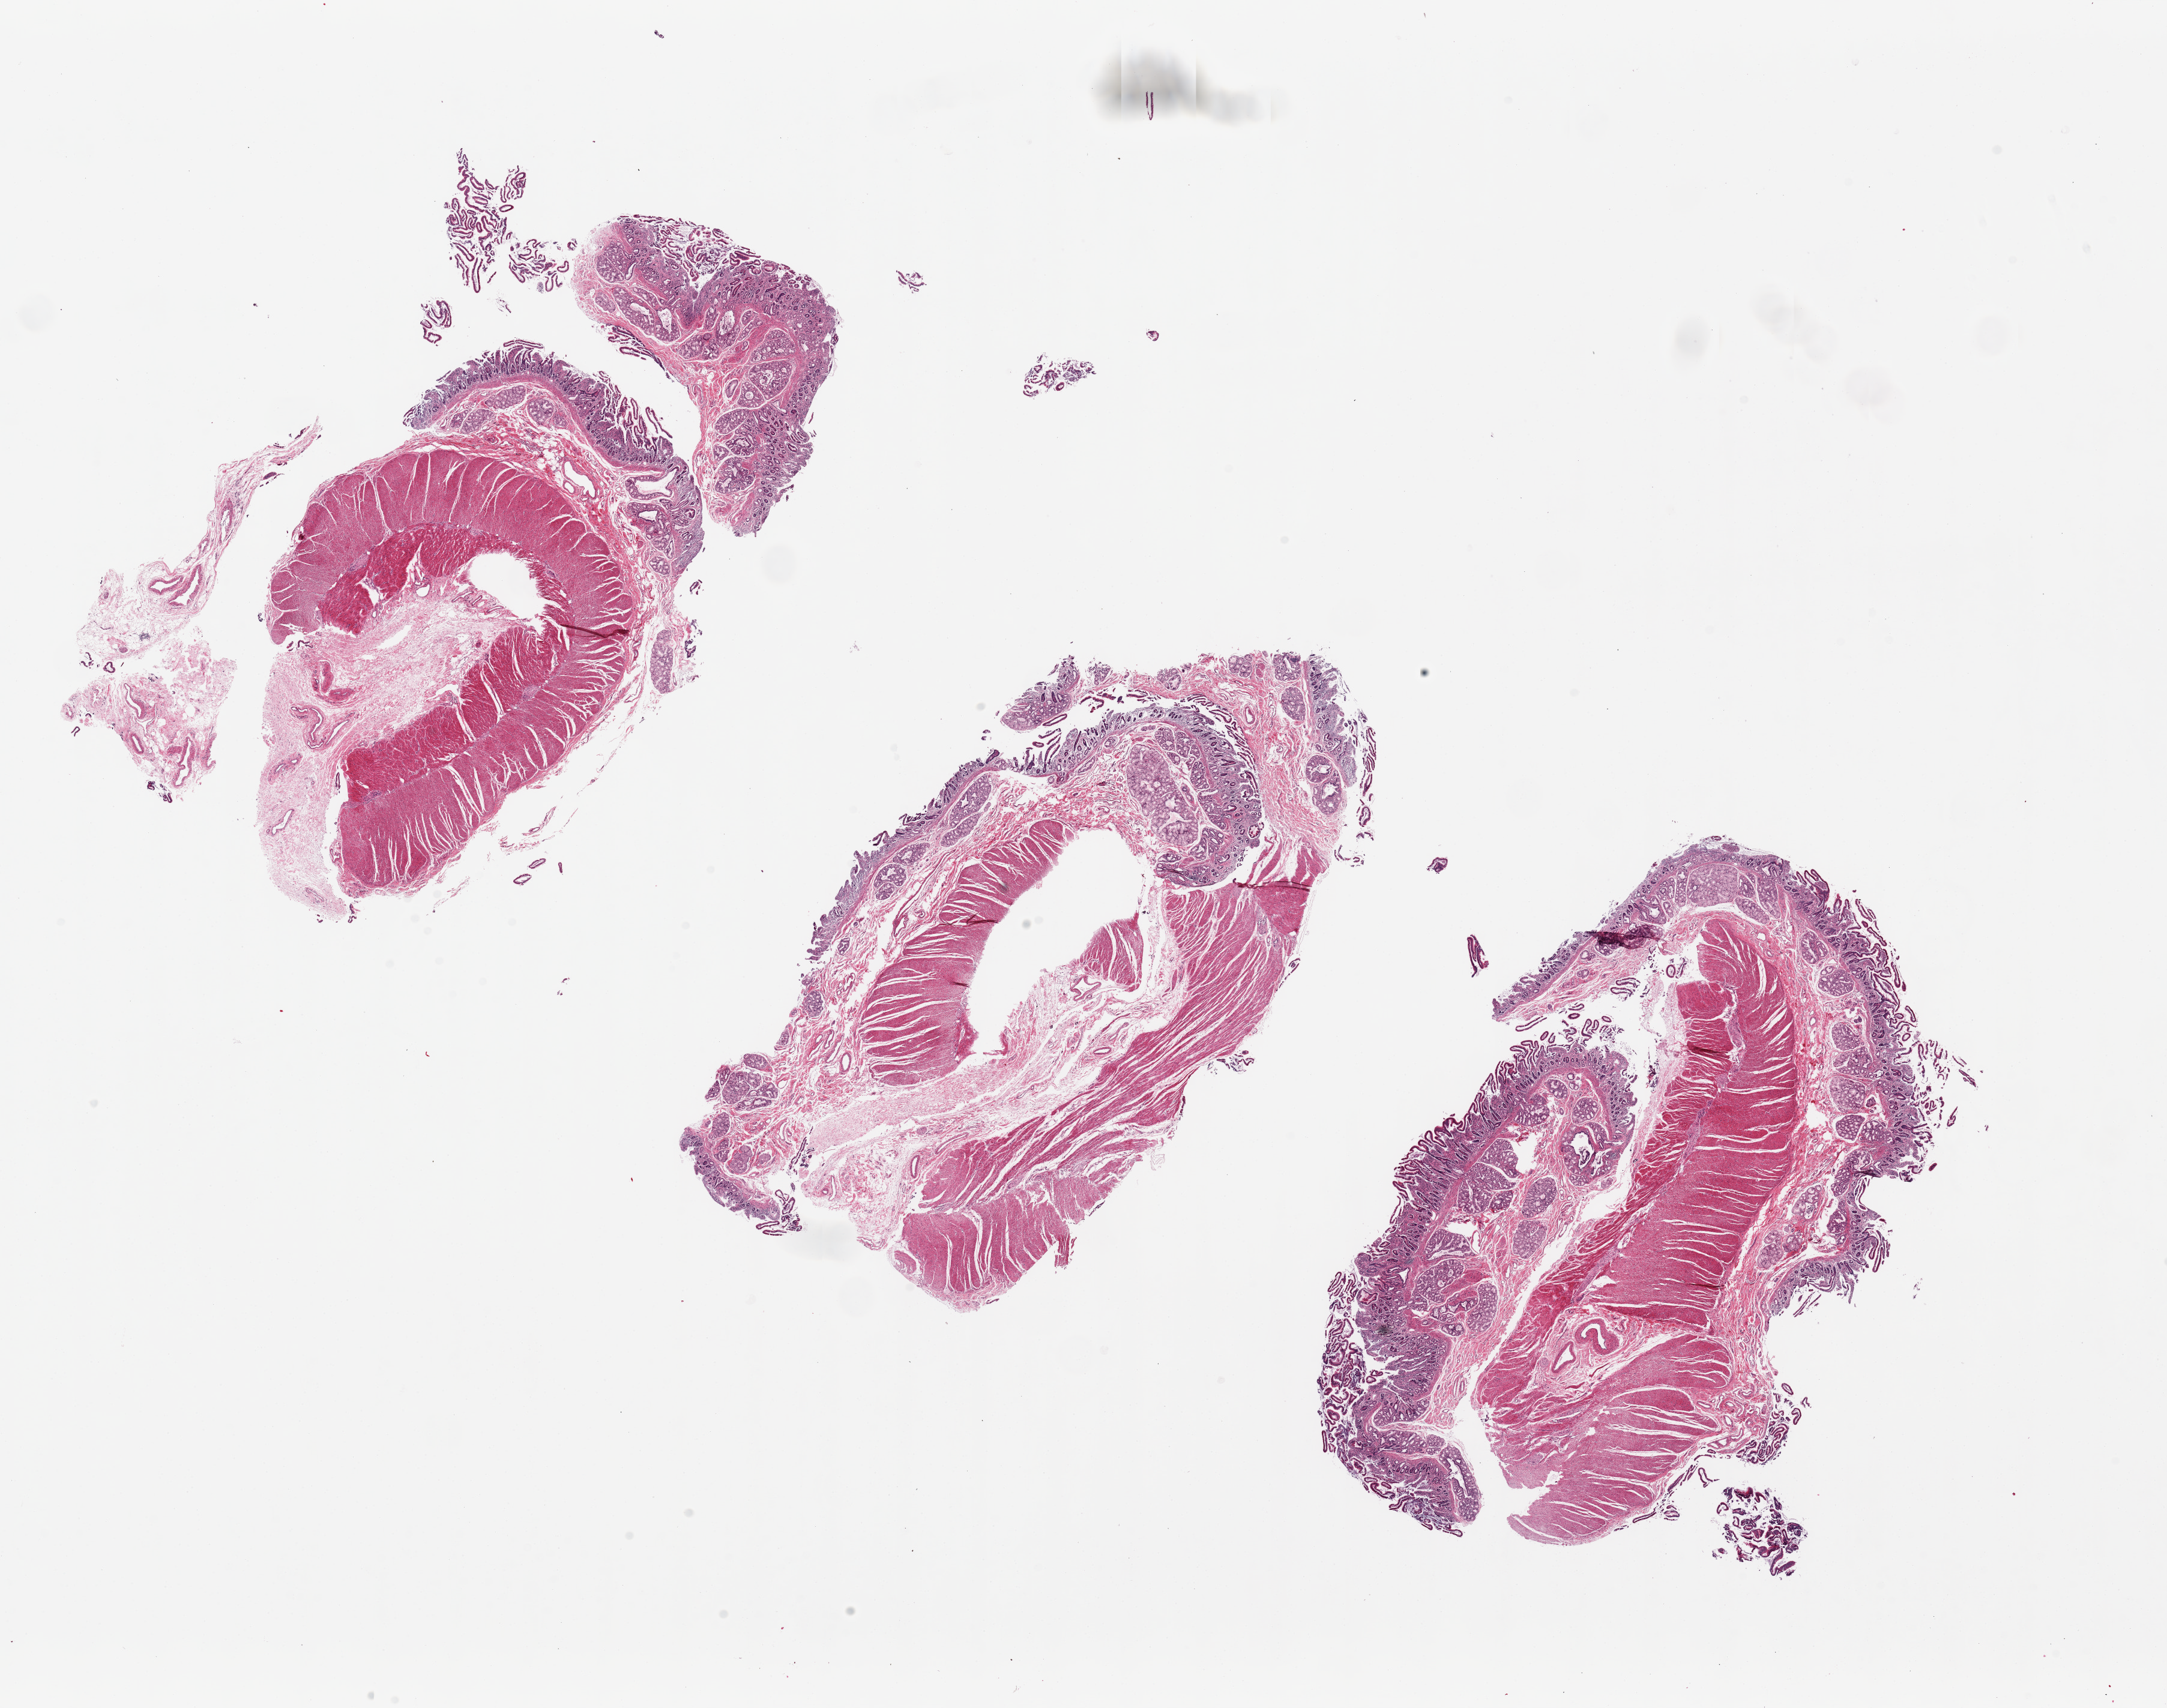
Whole-slide image, haematoxylin and eosin stain, shown as a low-resolution overview of the whole scanned area (about 28.5 x 22.5 mm), PAXgene-fixed, paraffin-embedded tissue, target tissue: ileum, donor tissue sample.
Review note (as recorded): 3 pieces, up to 11x7.5mm; duodenum, not ileum (contains Brunner glands) no lymphoid tissue; full thickness wall rather than mucosa.